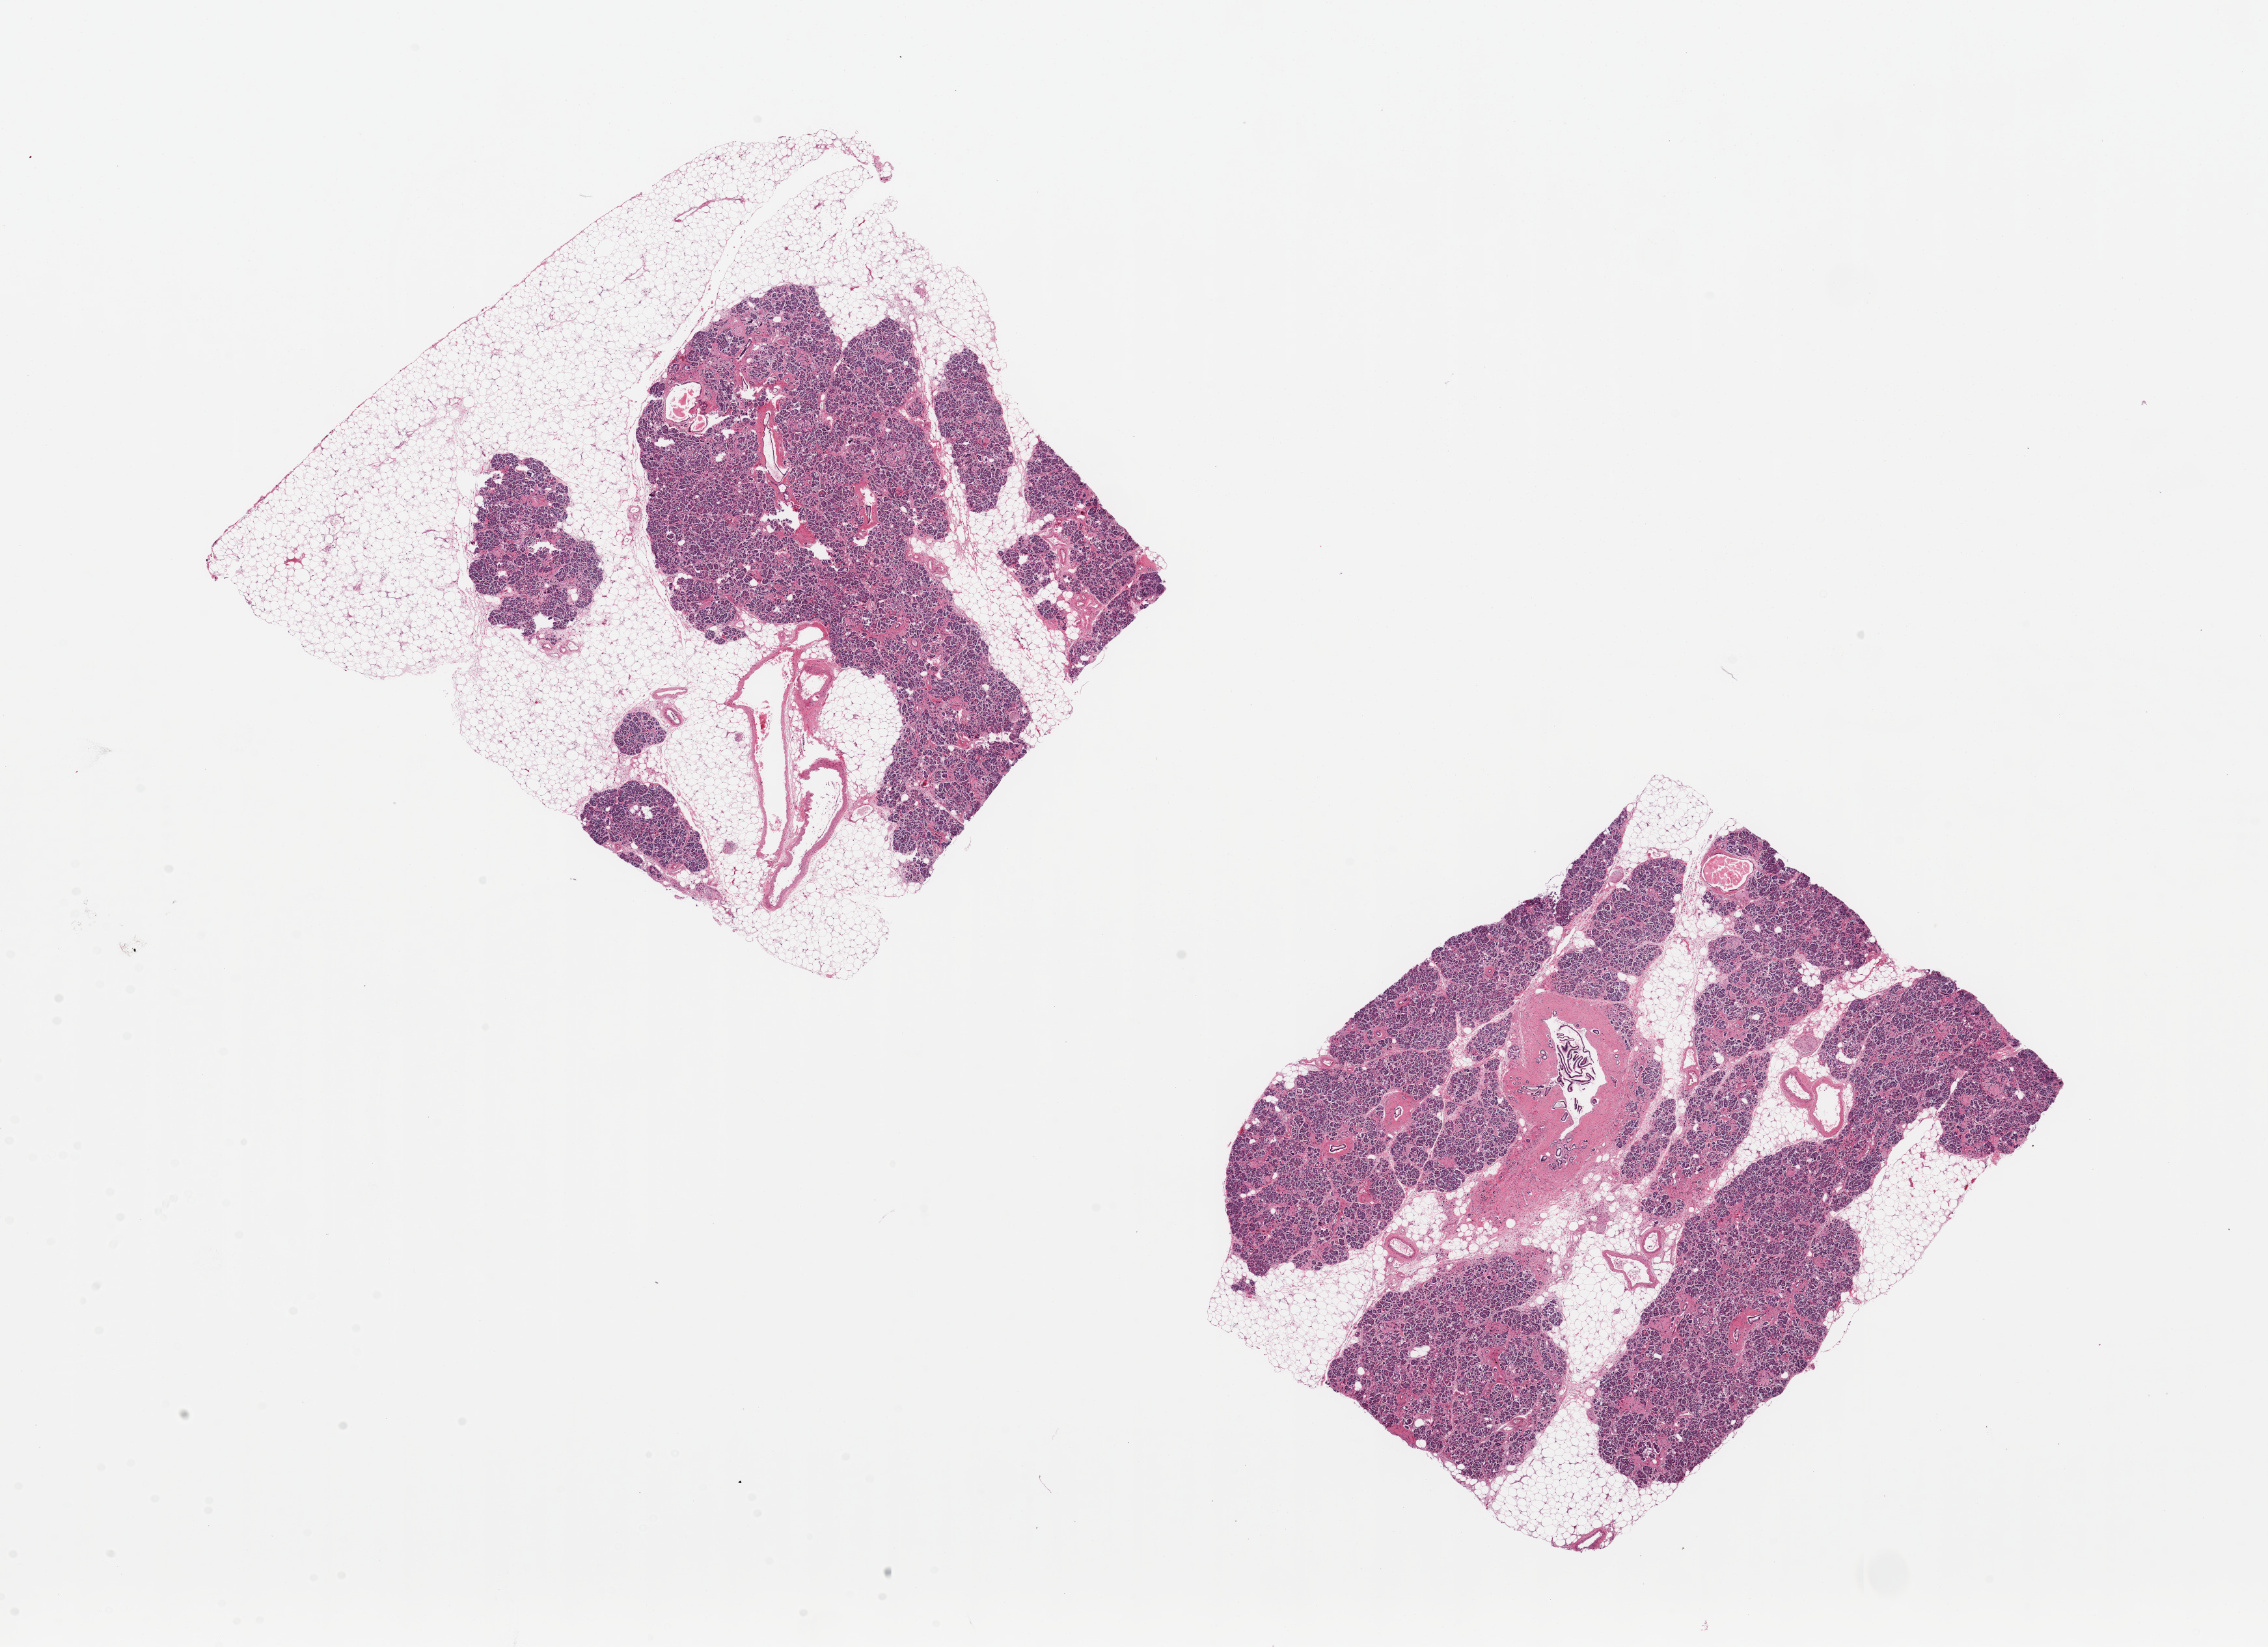
Digitized H&E-stained section — low-resolution overview of the scanned area, about 27.6 x 20.0 mm, PAXgene-fixed, paraffin-embedded tissue, sampled site (target tissue): pancreas, donor tissue sample. Male donor.
Review note (as recorded): 2 ~8x7mm pieces, each 40-50% adipose tissue, partly saponified.